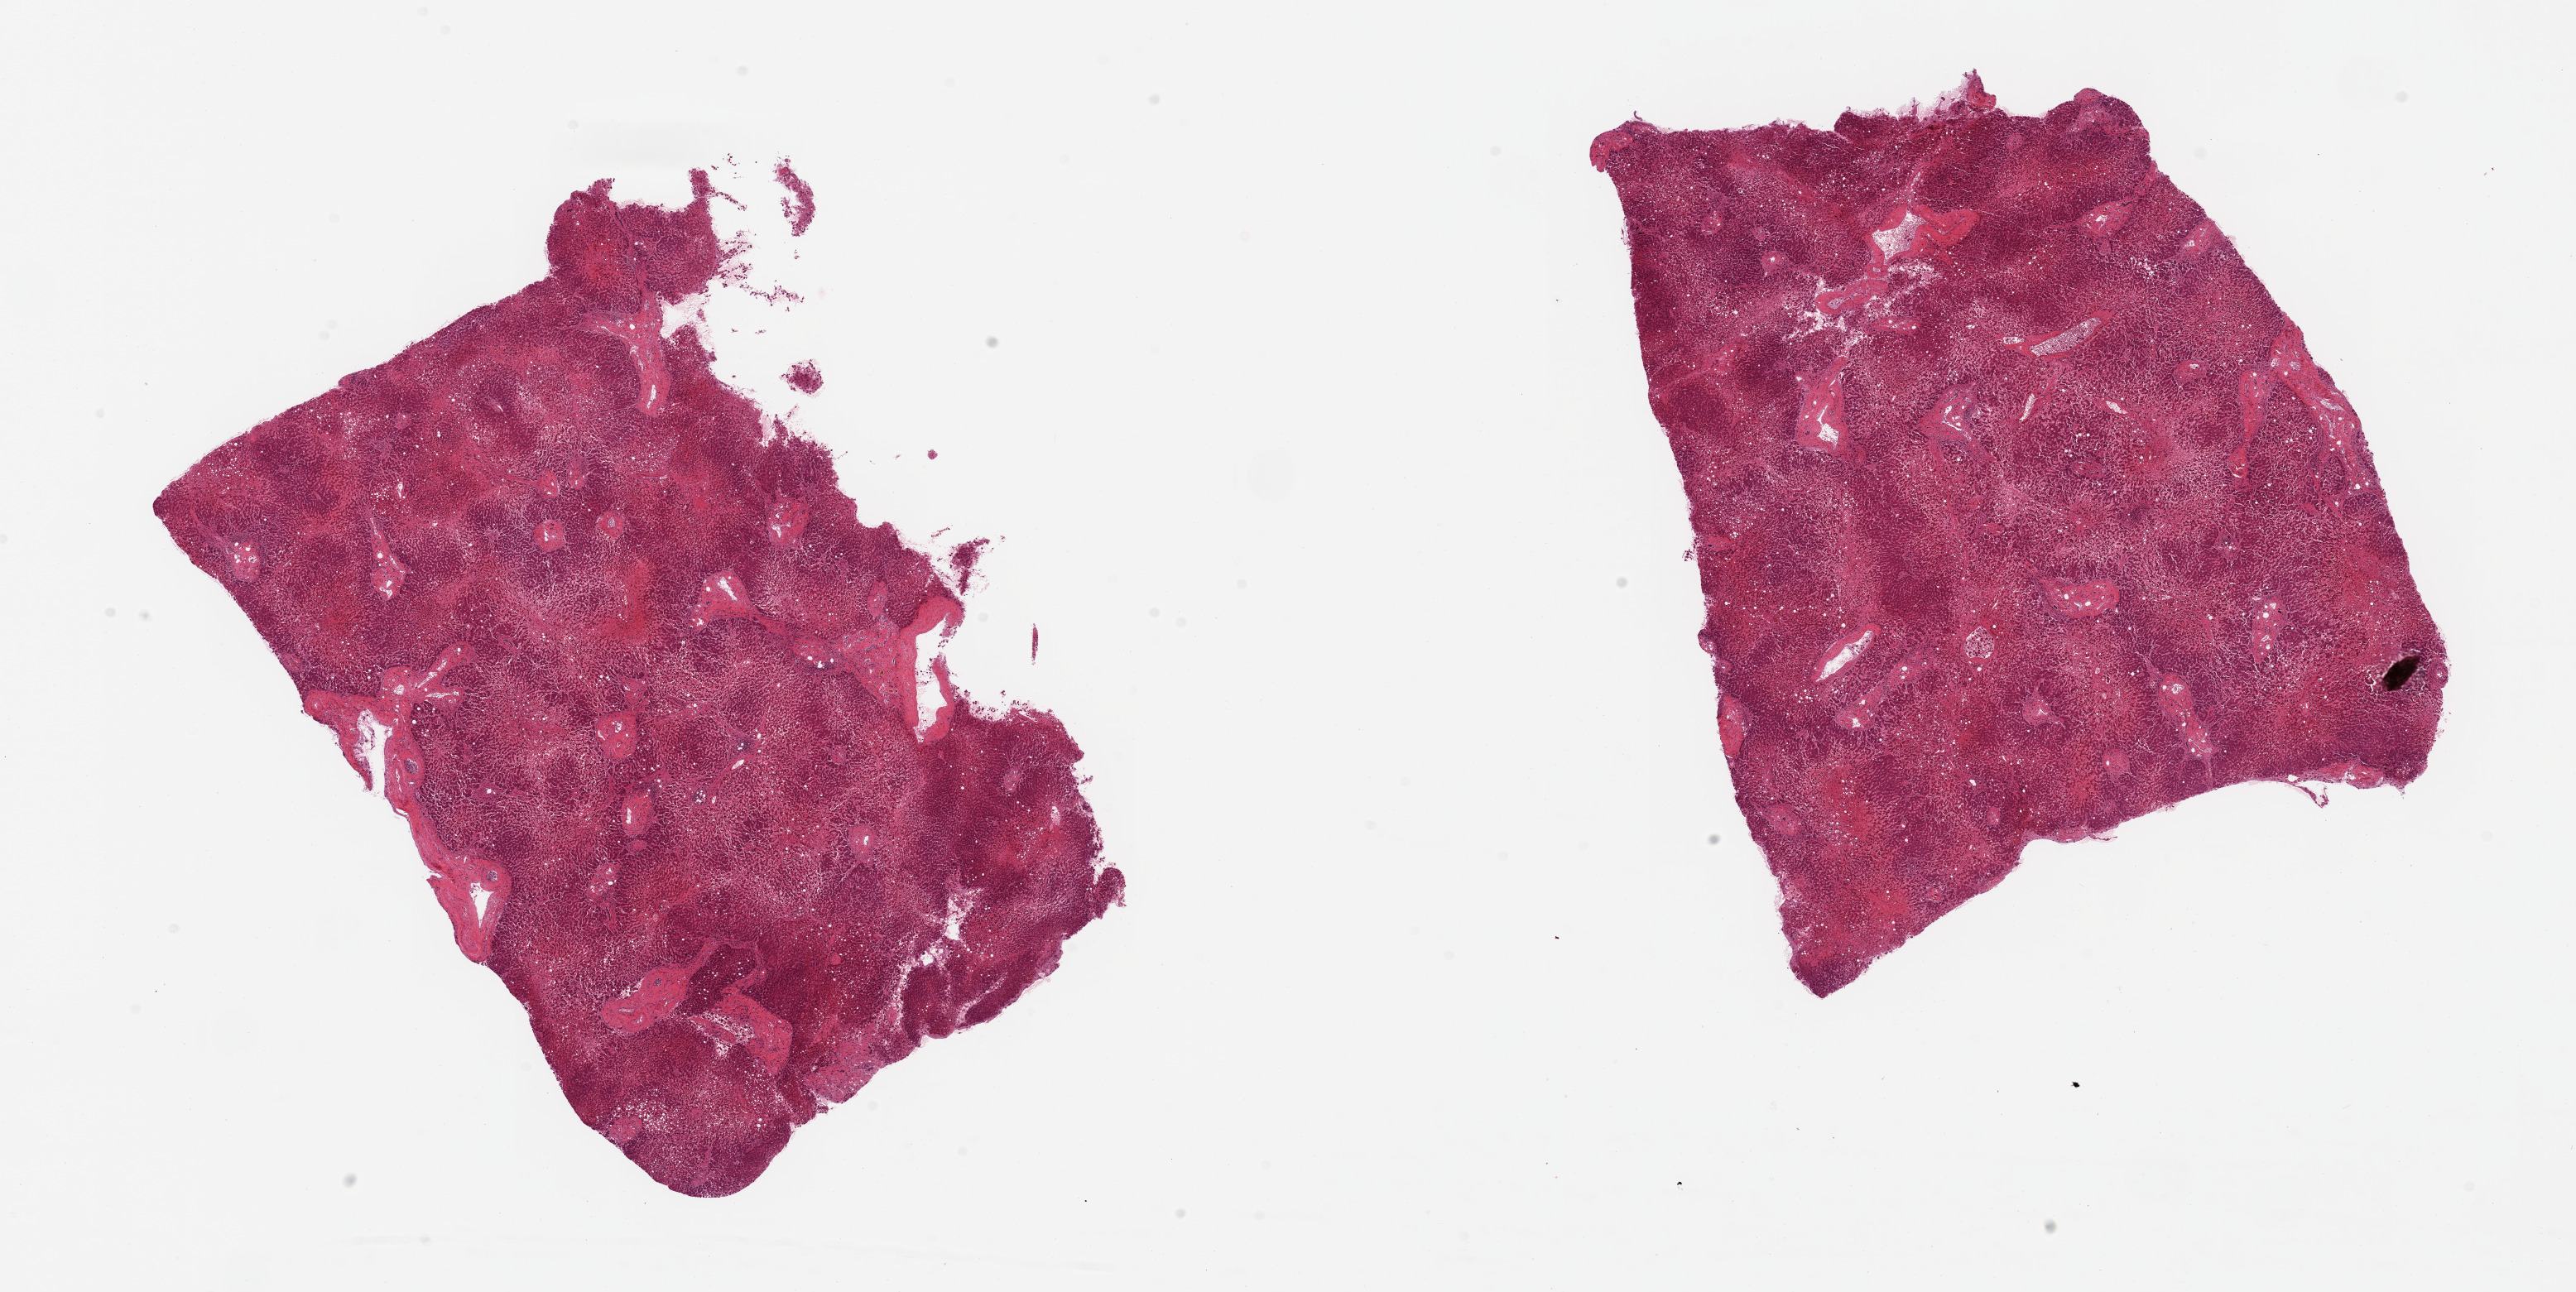
Digitized haematoxylin and eosin-stained section, a low-resolution overview of the entire scanned area, about 24.6 x 12.3 mm; PAXgene-fixed paraffin-embedded (PFPE) section; target tissue: liver; donor tissue sample. Donor: female.
Reviewer comment on this tissue sample: 2 pieces; severe central congestion and atrophy.